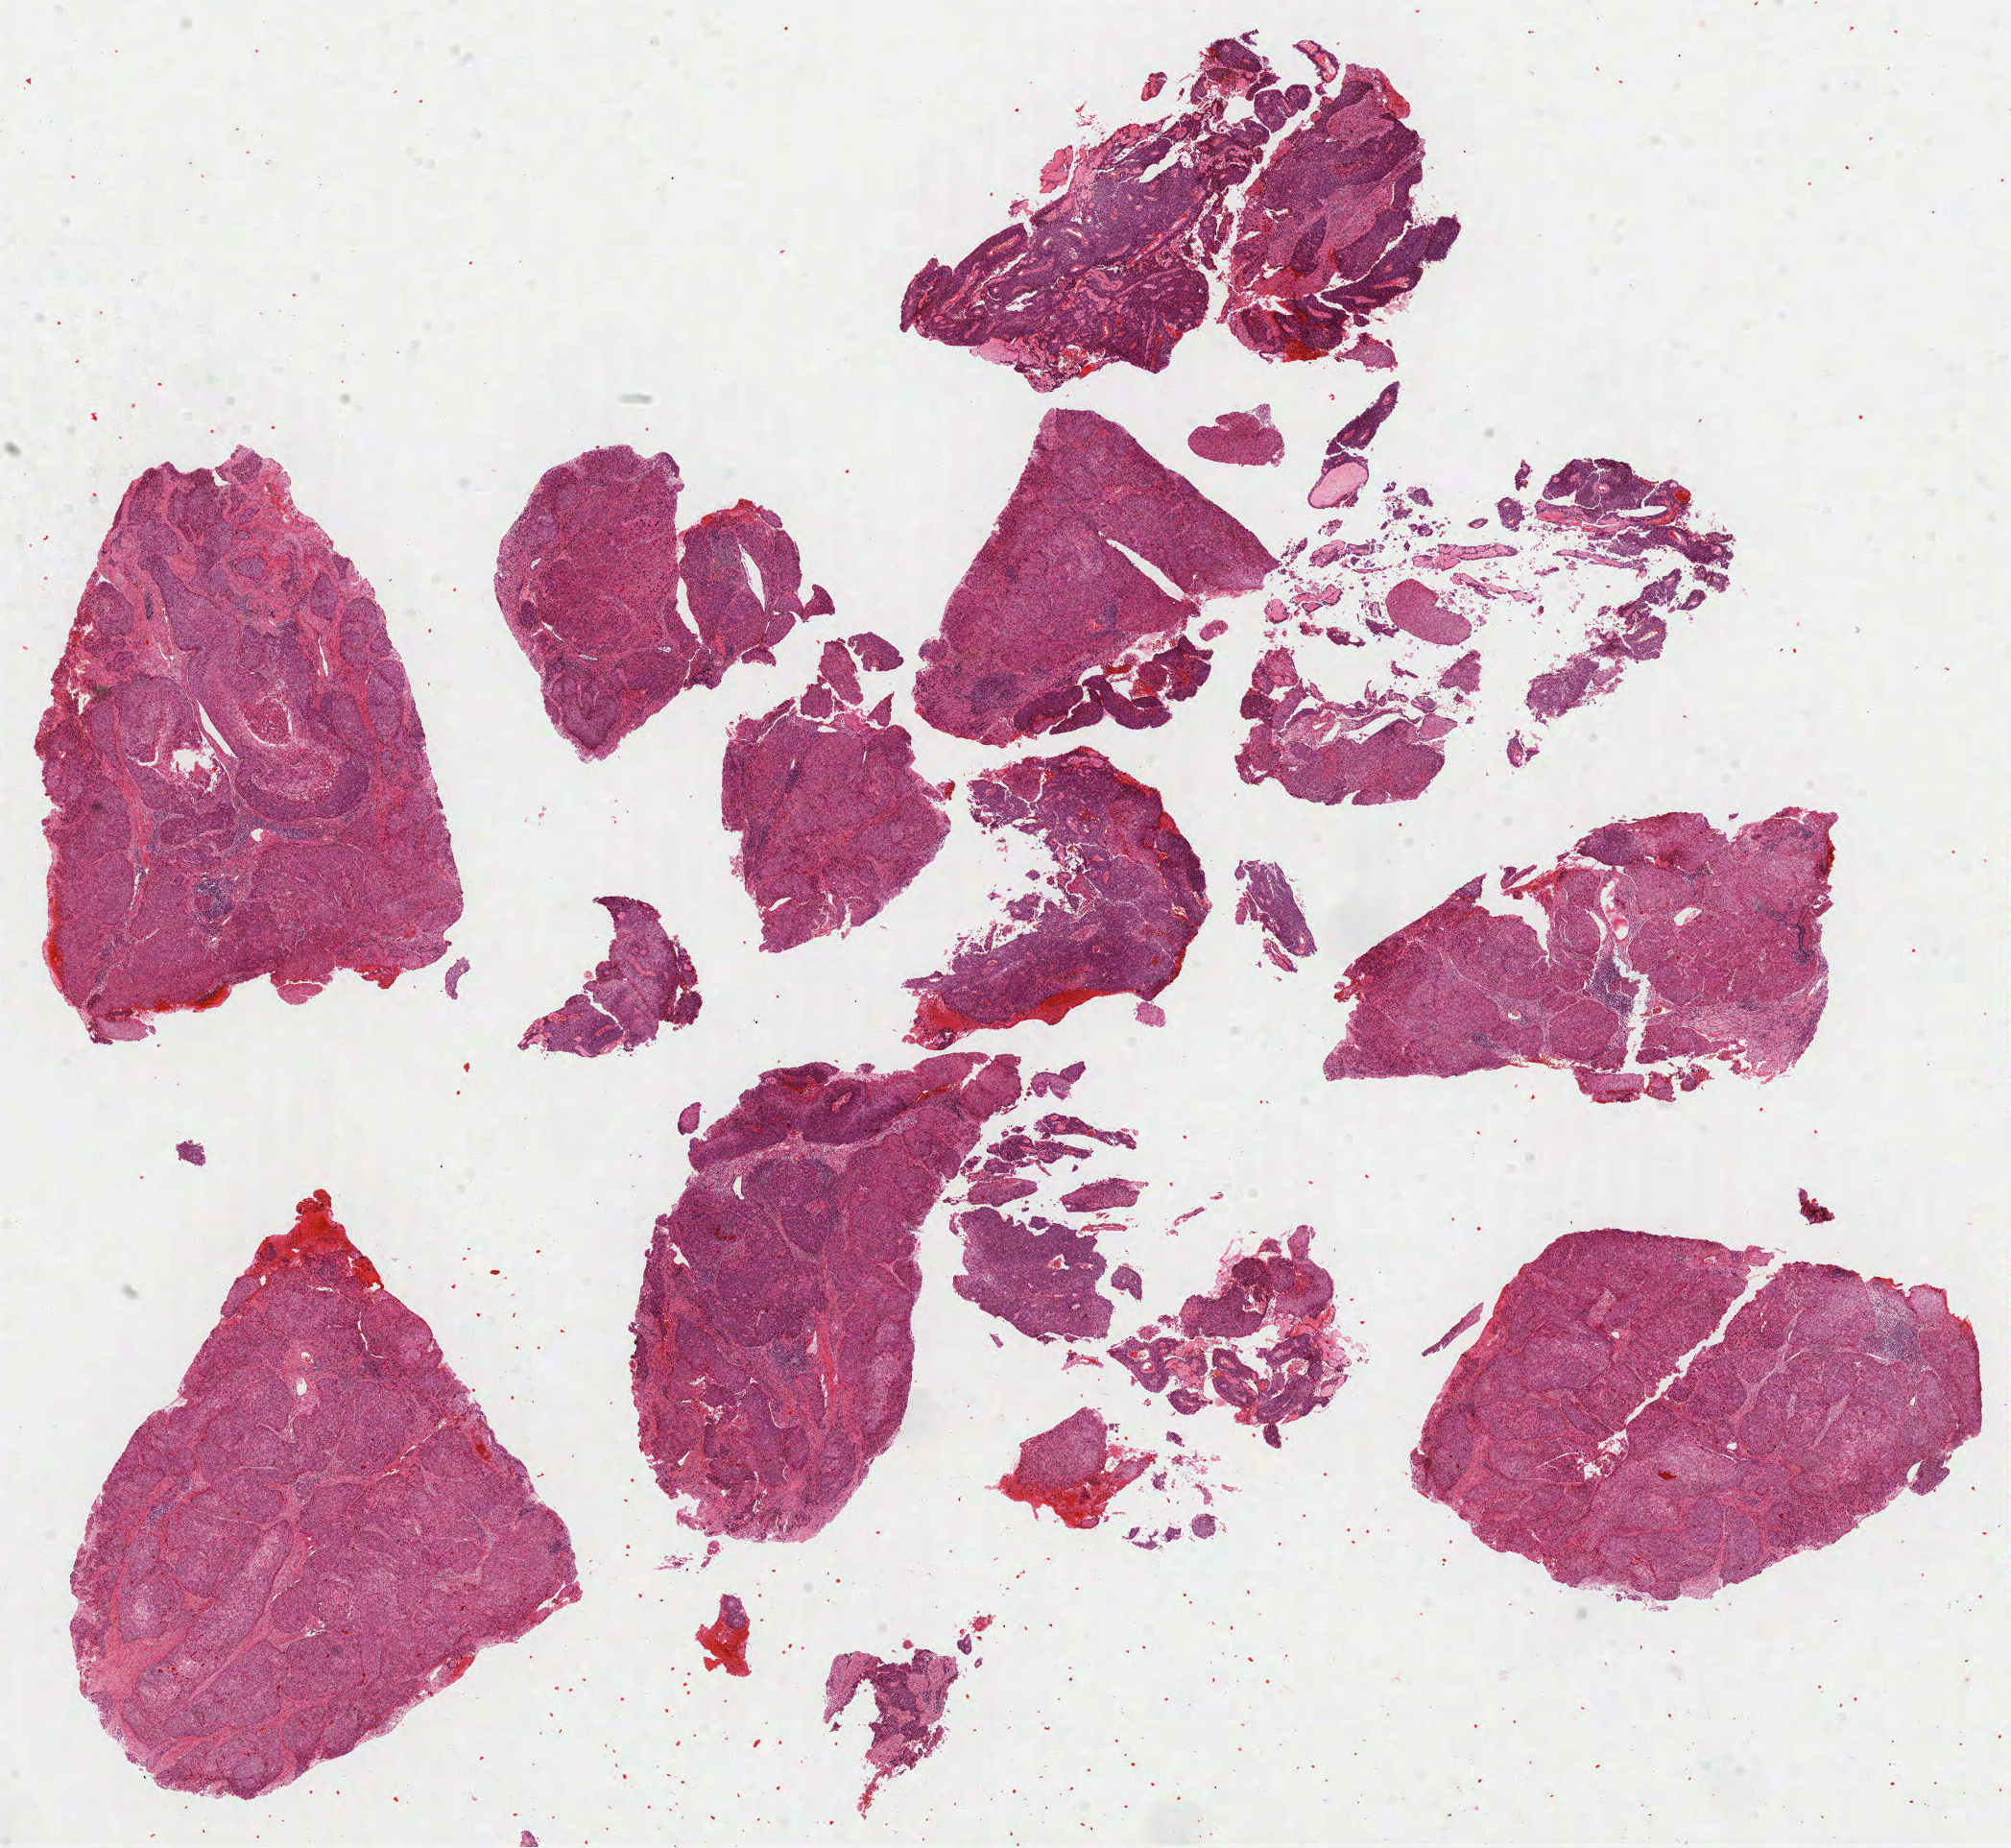
Hematoxylin and eosin (H&E) stained whole-slide image — whole scanned area (about 16.9 x 15.5 mm, slide scanned at 40x) shown as a low-resolution overview, formalin-fixed paraffin-embedded (FFPE) diagnostic section, primary tumour sample from the cervix. Patient: female, age at initial diagnosis 67 years.
Diagnosis: Squamous cell carcinoma, large cell, nonkeratinizing, NOS (cervix uteri).